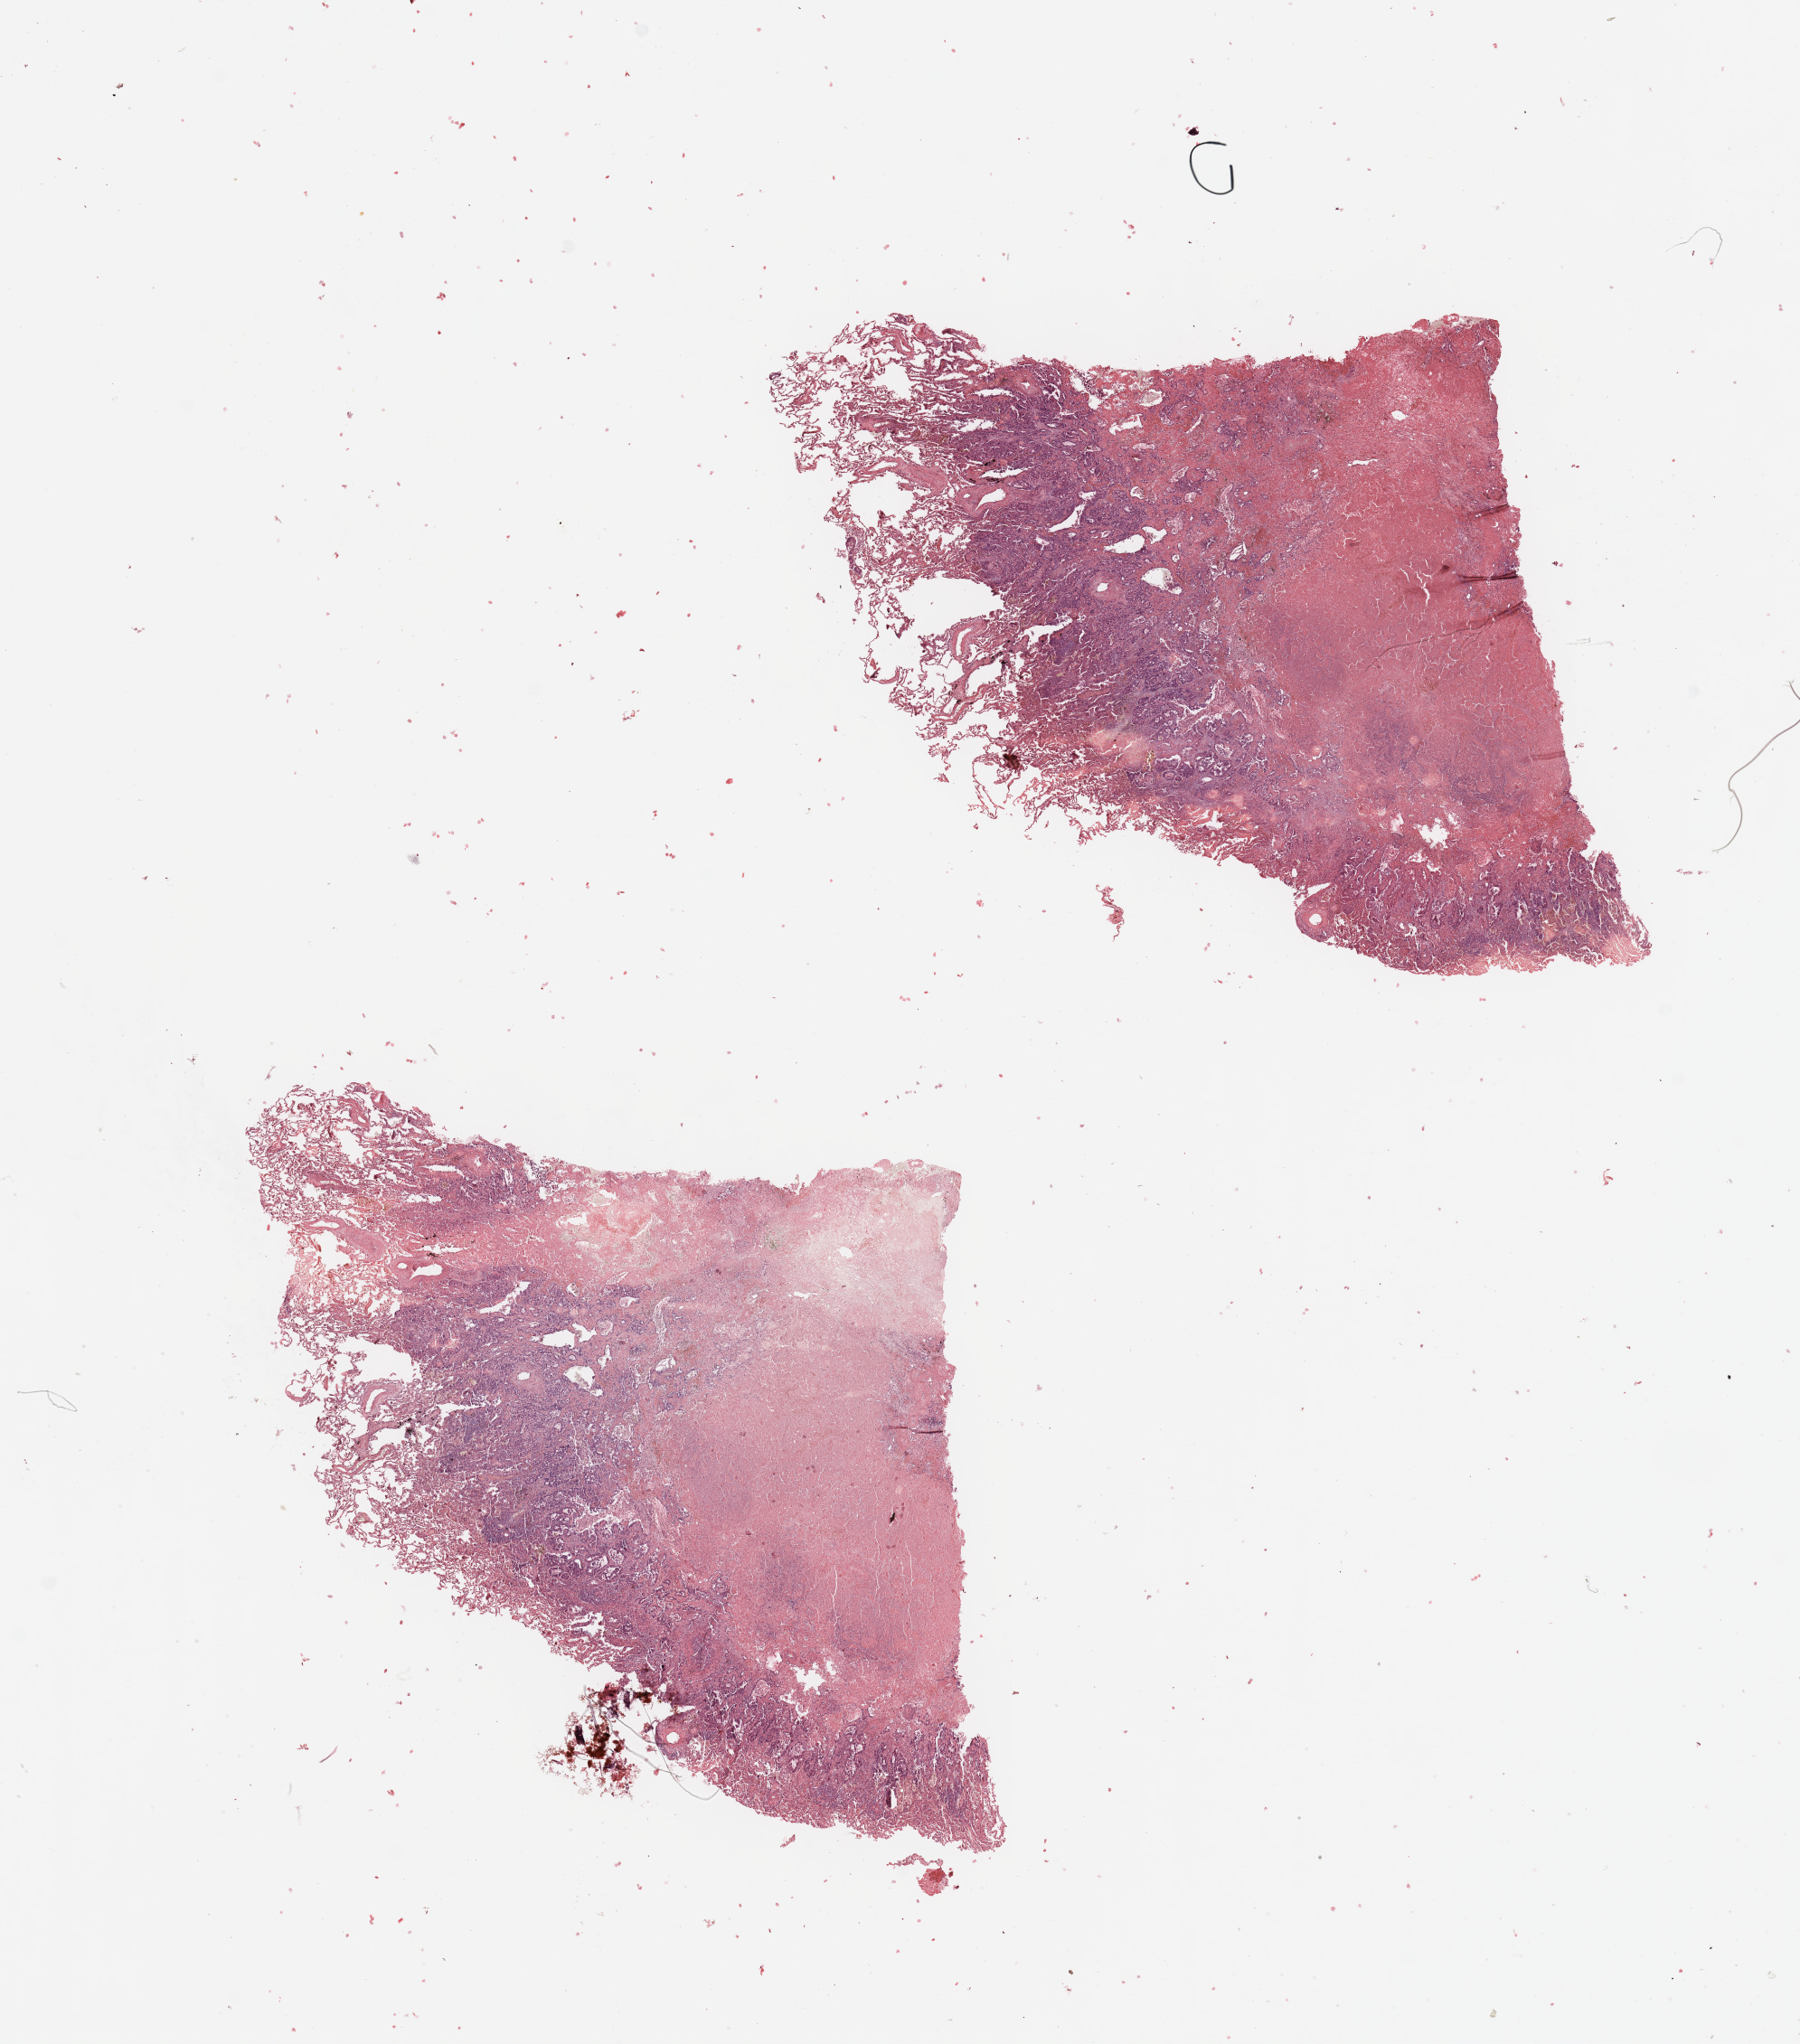
H&E whole-slide image, shown as a low-resolution overview of the whole scanned area (about 15.8 x 17.9 mm, acquisition: 20x scan), tumour tissue sample, lung. Male, 69 y/o.
Histologic diagnosis: Adenocarcinoma, NOS.